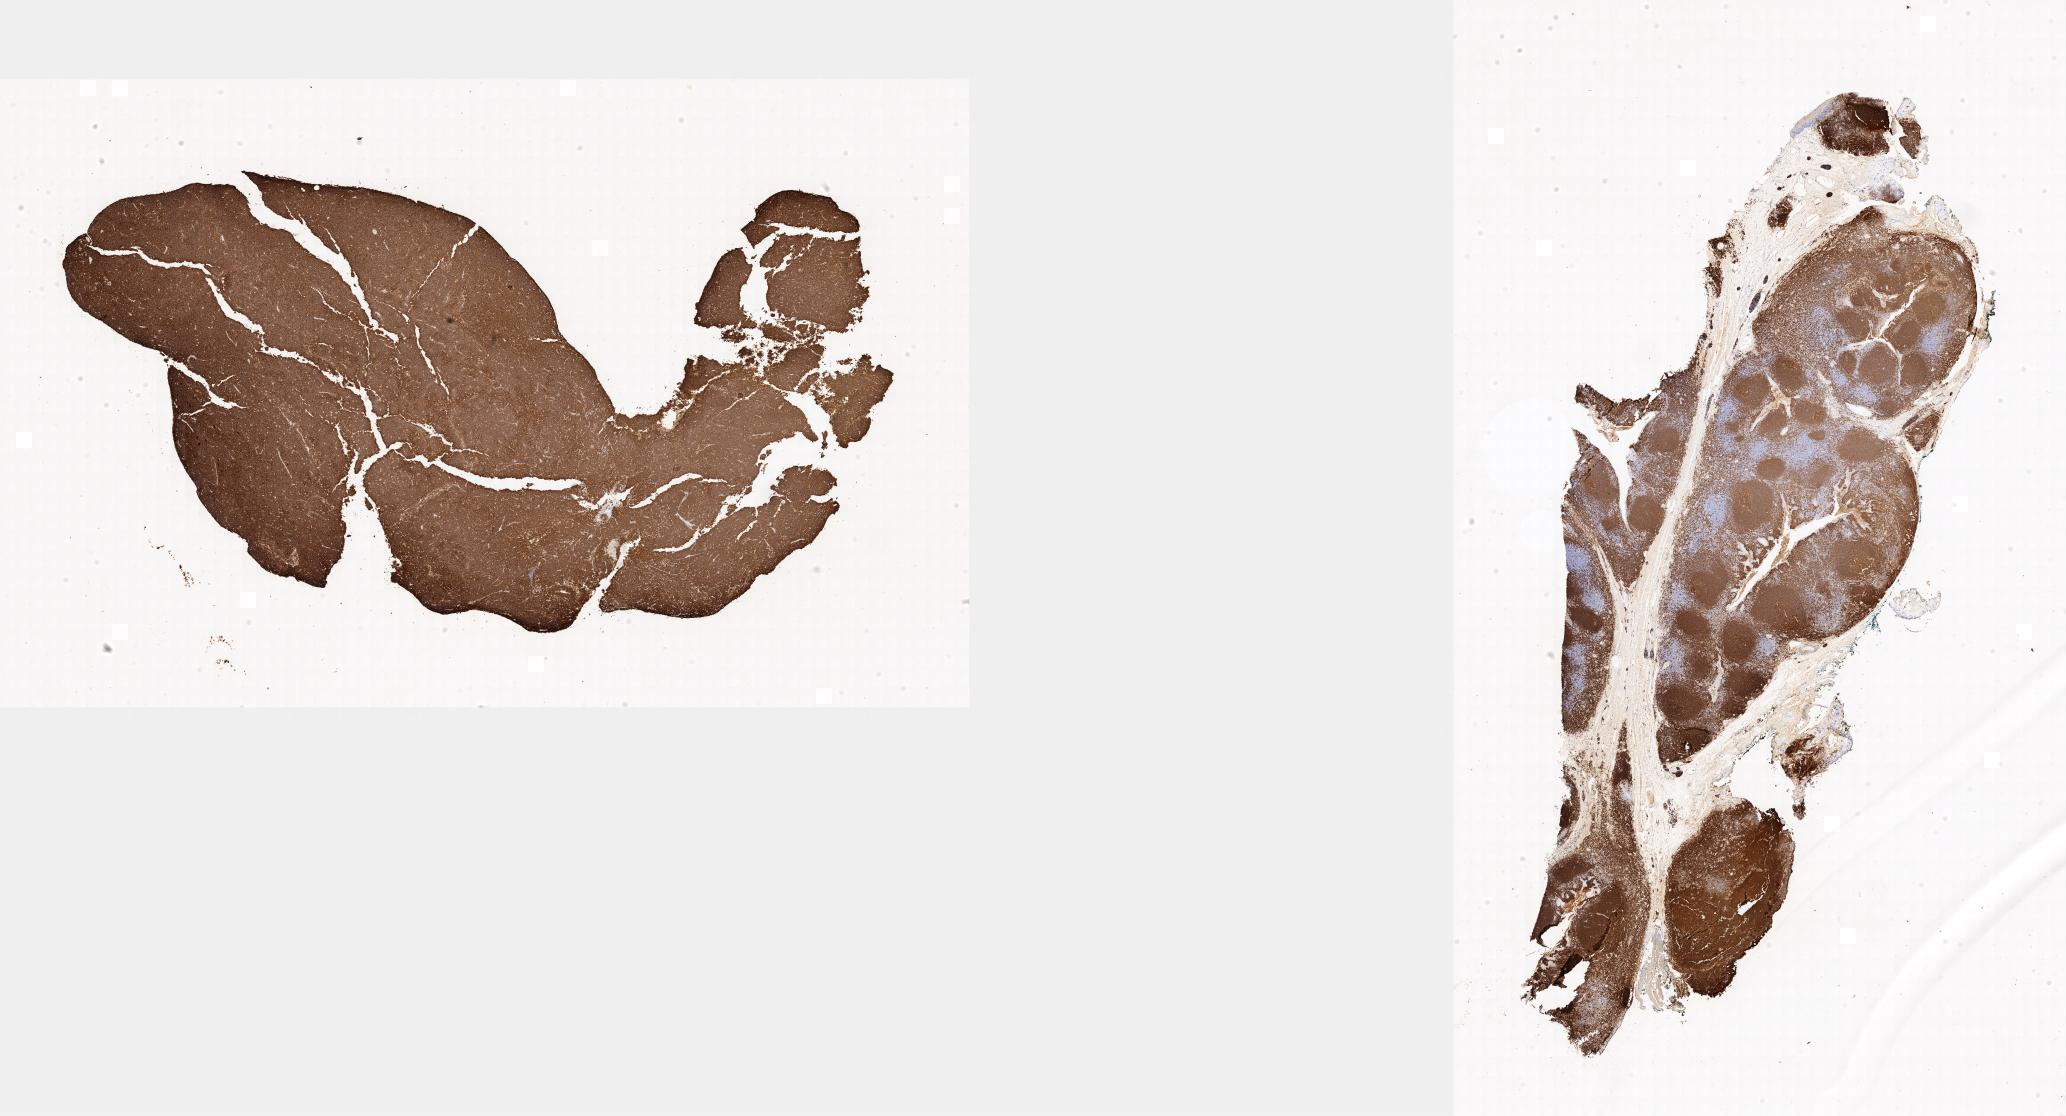
Immunohistochemistry (IHC) whole-slide image stained for CD20 — shown as a low-resolution overview of the whole scanned area; tumor tissue; anatomic site: lymph node of head and neck. Patient: male, age at initial diagnosis 5 years.
Histologic diagnosis: Burkitt lymphoma, NOS.